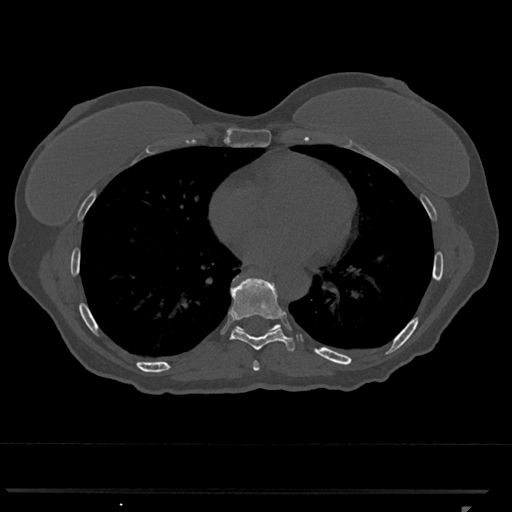
CT including the spine, one axial slice; slice 658 of 793 in the series (ordered by position); reconstruction kernel Br40s/3; 120 kVp; bone window (W 1800 / L 400 HU); 0.5 mm slice thickness; 512 × 512 image matrix, field of view 380 × 380 mm. Patient: female, 62 years. From the clinical record (not read from this slice): primary cancer: renal.
Annotated regions visible in this slice (semi-automatically segmented with operator editing):
- T7 vertebra: box from (x=253, y=361) to (x=260, y=371) px
- T8 vertebra: (x=230, y=279)–(x=302, y=351)
- T9 vertebra: (x=233, y=276)–(x=281, y=331)